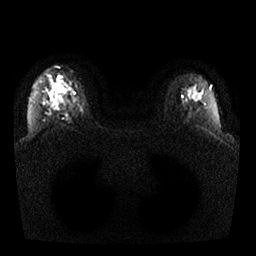
Breast MRI, one axial slice; diffusion-weighted series; image 2 of 4 stored at this slice position (different b-values; order by instance number); 1.5 T; 4 mm slice thickness; 256 × 256 image matrix. Female patient.
Structures marked on this image (outlined manually by an expert reader):
- tumour on diffusion-weighted imaging: bounding box (x1, y1, x2, y2) in pixels: (50, 102, 55, 108)